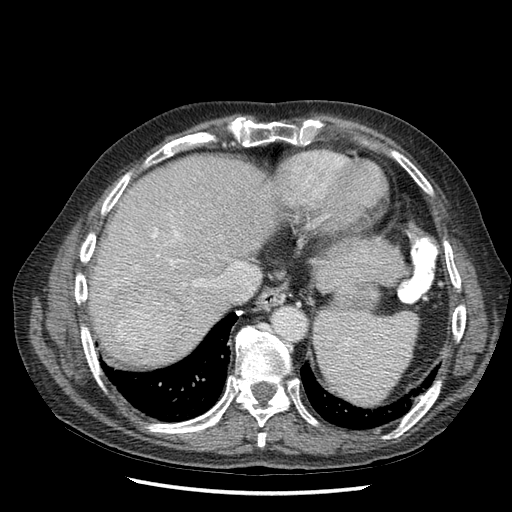
Contrast-enhanced abdominal CT (liver protocol), one axial slice. Slice 55 of 67 in the series (ordered by position). Reconstruction kernel STANDARD. Soft-tissue window (W 400 / L 40 HU). 512 × 512 image matrix, field of view 360 × 360 mm. Case-level facts recorded for this patient, not image findings: diagnosis: hepatocellular carcinoma (patient treated with transarterial chemoembolisation; whether this scan precedes or follows treatment is not stated here); TNM stage (as recorded): Stage-I; Child-Pugh class: A; tumour differentiation: moderately differentiated; tumour nodularity: uninodular.
Structures marked on this image (semi-automatically segmented with operator editing):
- abdominal aorta: bounding box (x1, y1, x2, y2) in pixels: (273, 306, 305, 337)
- liver parenchyma outside the tumour (the mass and vessels are separate outlines, so this box may not span the whole liver): (89, 154, 274, 362)
- mass: (109, 284, 181, 357)
- liver vessels: (133, 228, 178, 268)